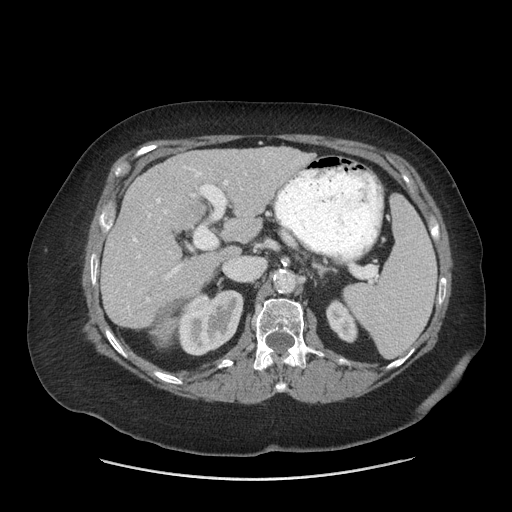
Contrast-enhanced abdominal CT (liver protocol), one axial slice; position 36 of 69 along the scan axis; 140 kVp; soft-tissue window (W 400 / L 40 HU); 2.5 mm slice thickness; 512 × 512 image matrix, field of view 420 × 420 mm. From the clinical record (not read from this slice): diagnosis: hepatocellular carcinoma (patient treated with transarterial chemoembolisation; whether this scan precedes or follows treatment is not stated here); TNM stage (as recorded): Stage-IIIB; Child-Pugh class: A; tumour nodularity: multinodular.
Outlined on this slice (semi-automatically segmented with operator editing):
- liver parenchyma outside the tumour (the mass and vessels are separate outlines, so this box may not span the whole liver): bounding box [x1, y1, x2, y2] px = [100, 146, 312, 328]
- mass: [153, 319, 175, 341]
- liver vessels: [127, 161, 264, 309]